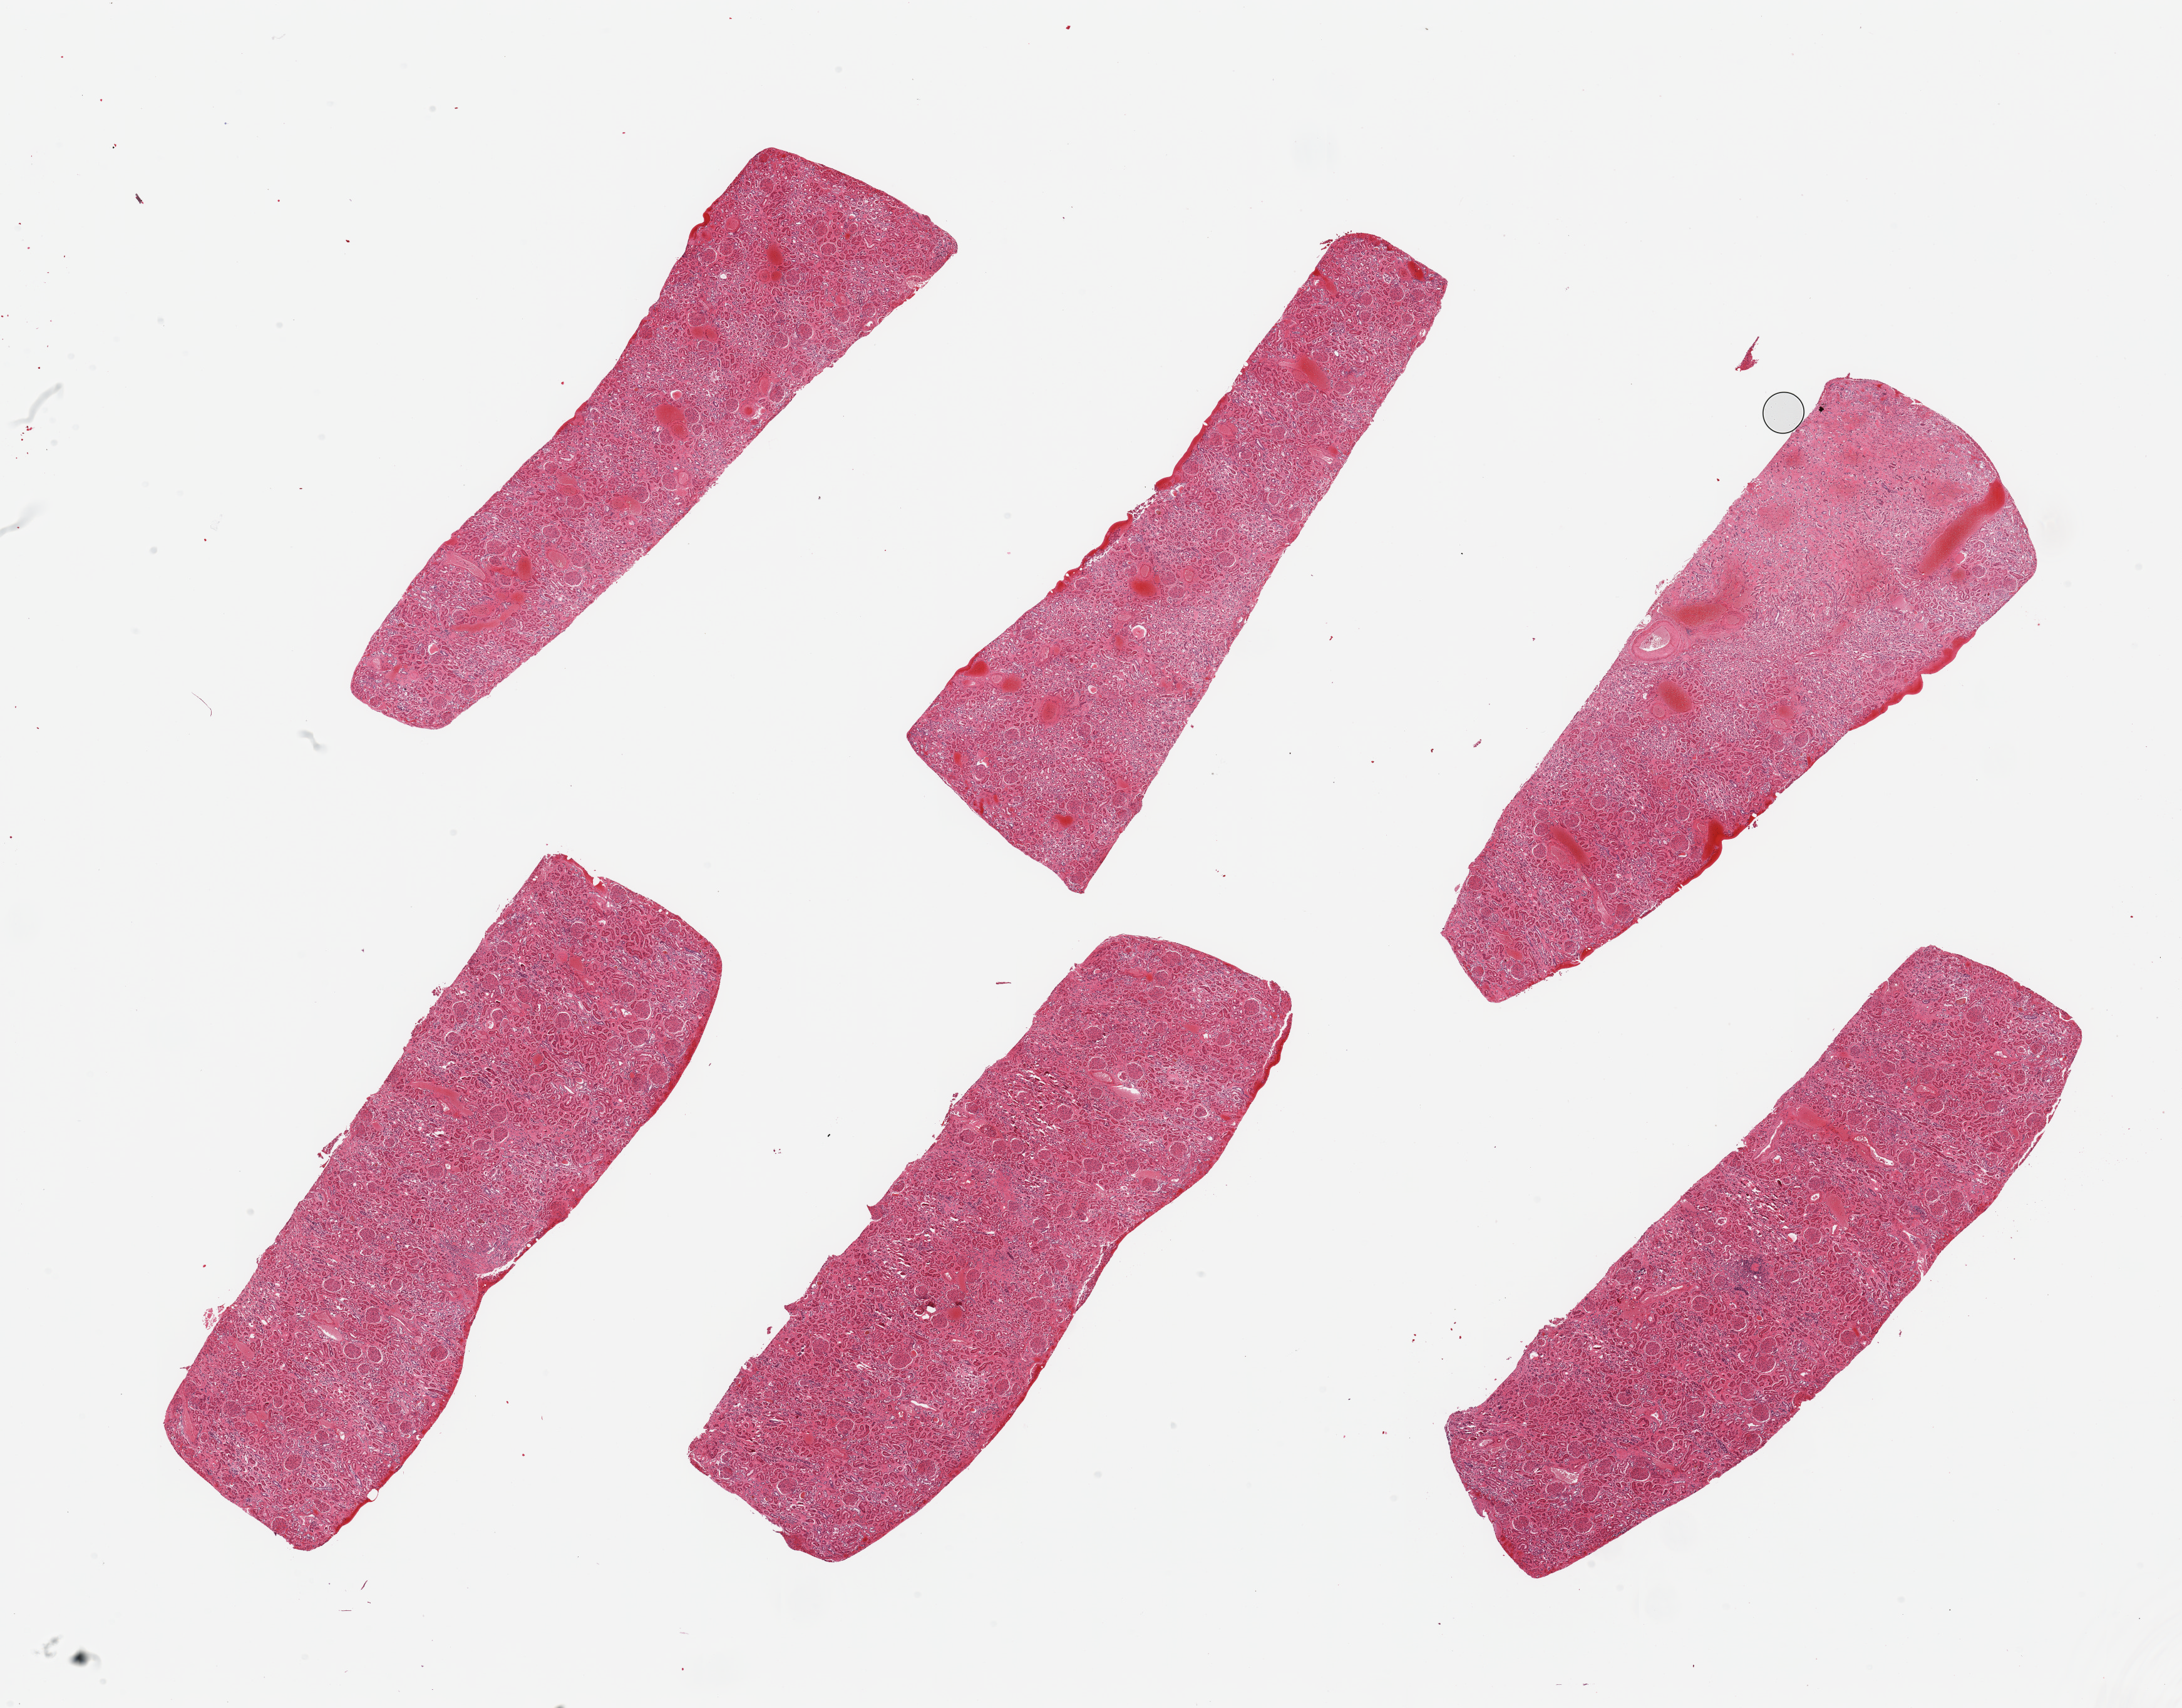
H&E whole-slide image, whole scanned area (about 27.6 x 21.6 mm) shown as a low-resolution overview, PAXgene-fixed, paraffin-embedded tissue, sampled site (target tissue): renal cortex, tissue donor sample. Donor sex: male.
Pathologist's review note for this sample: 6 pieces, glomeruli present, advanced tubular autolysis.